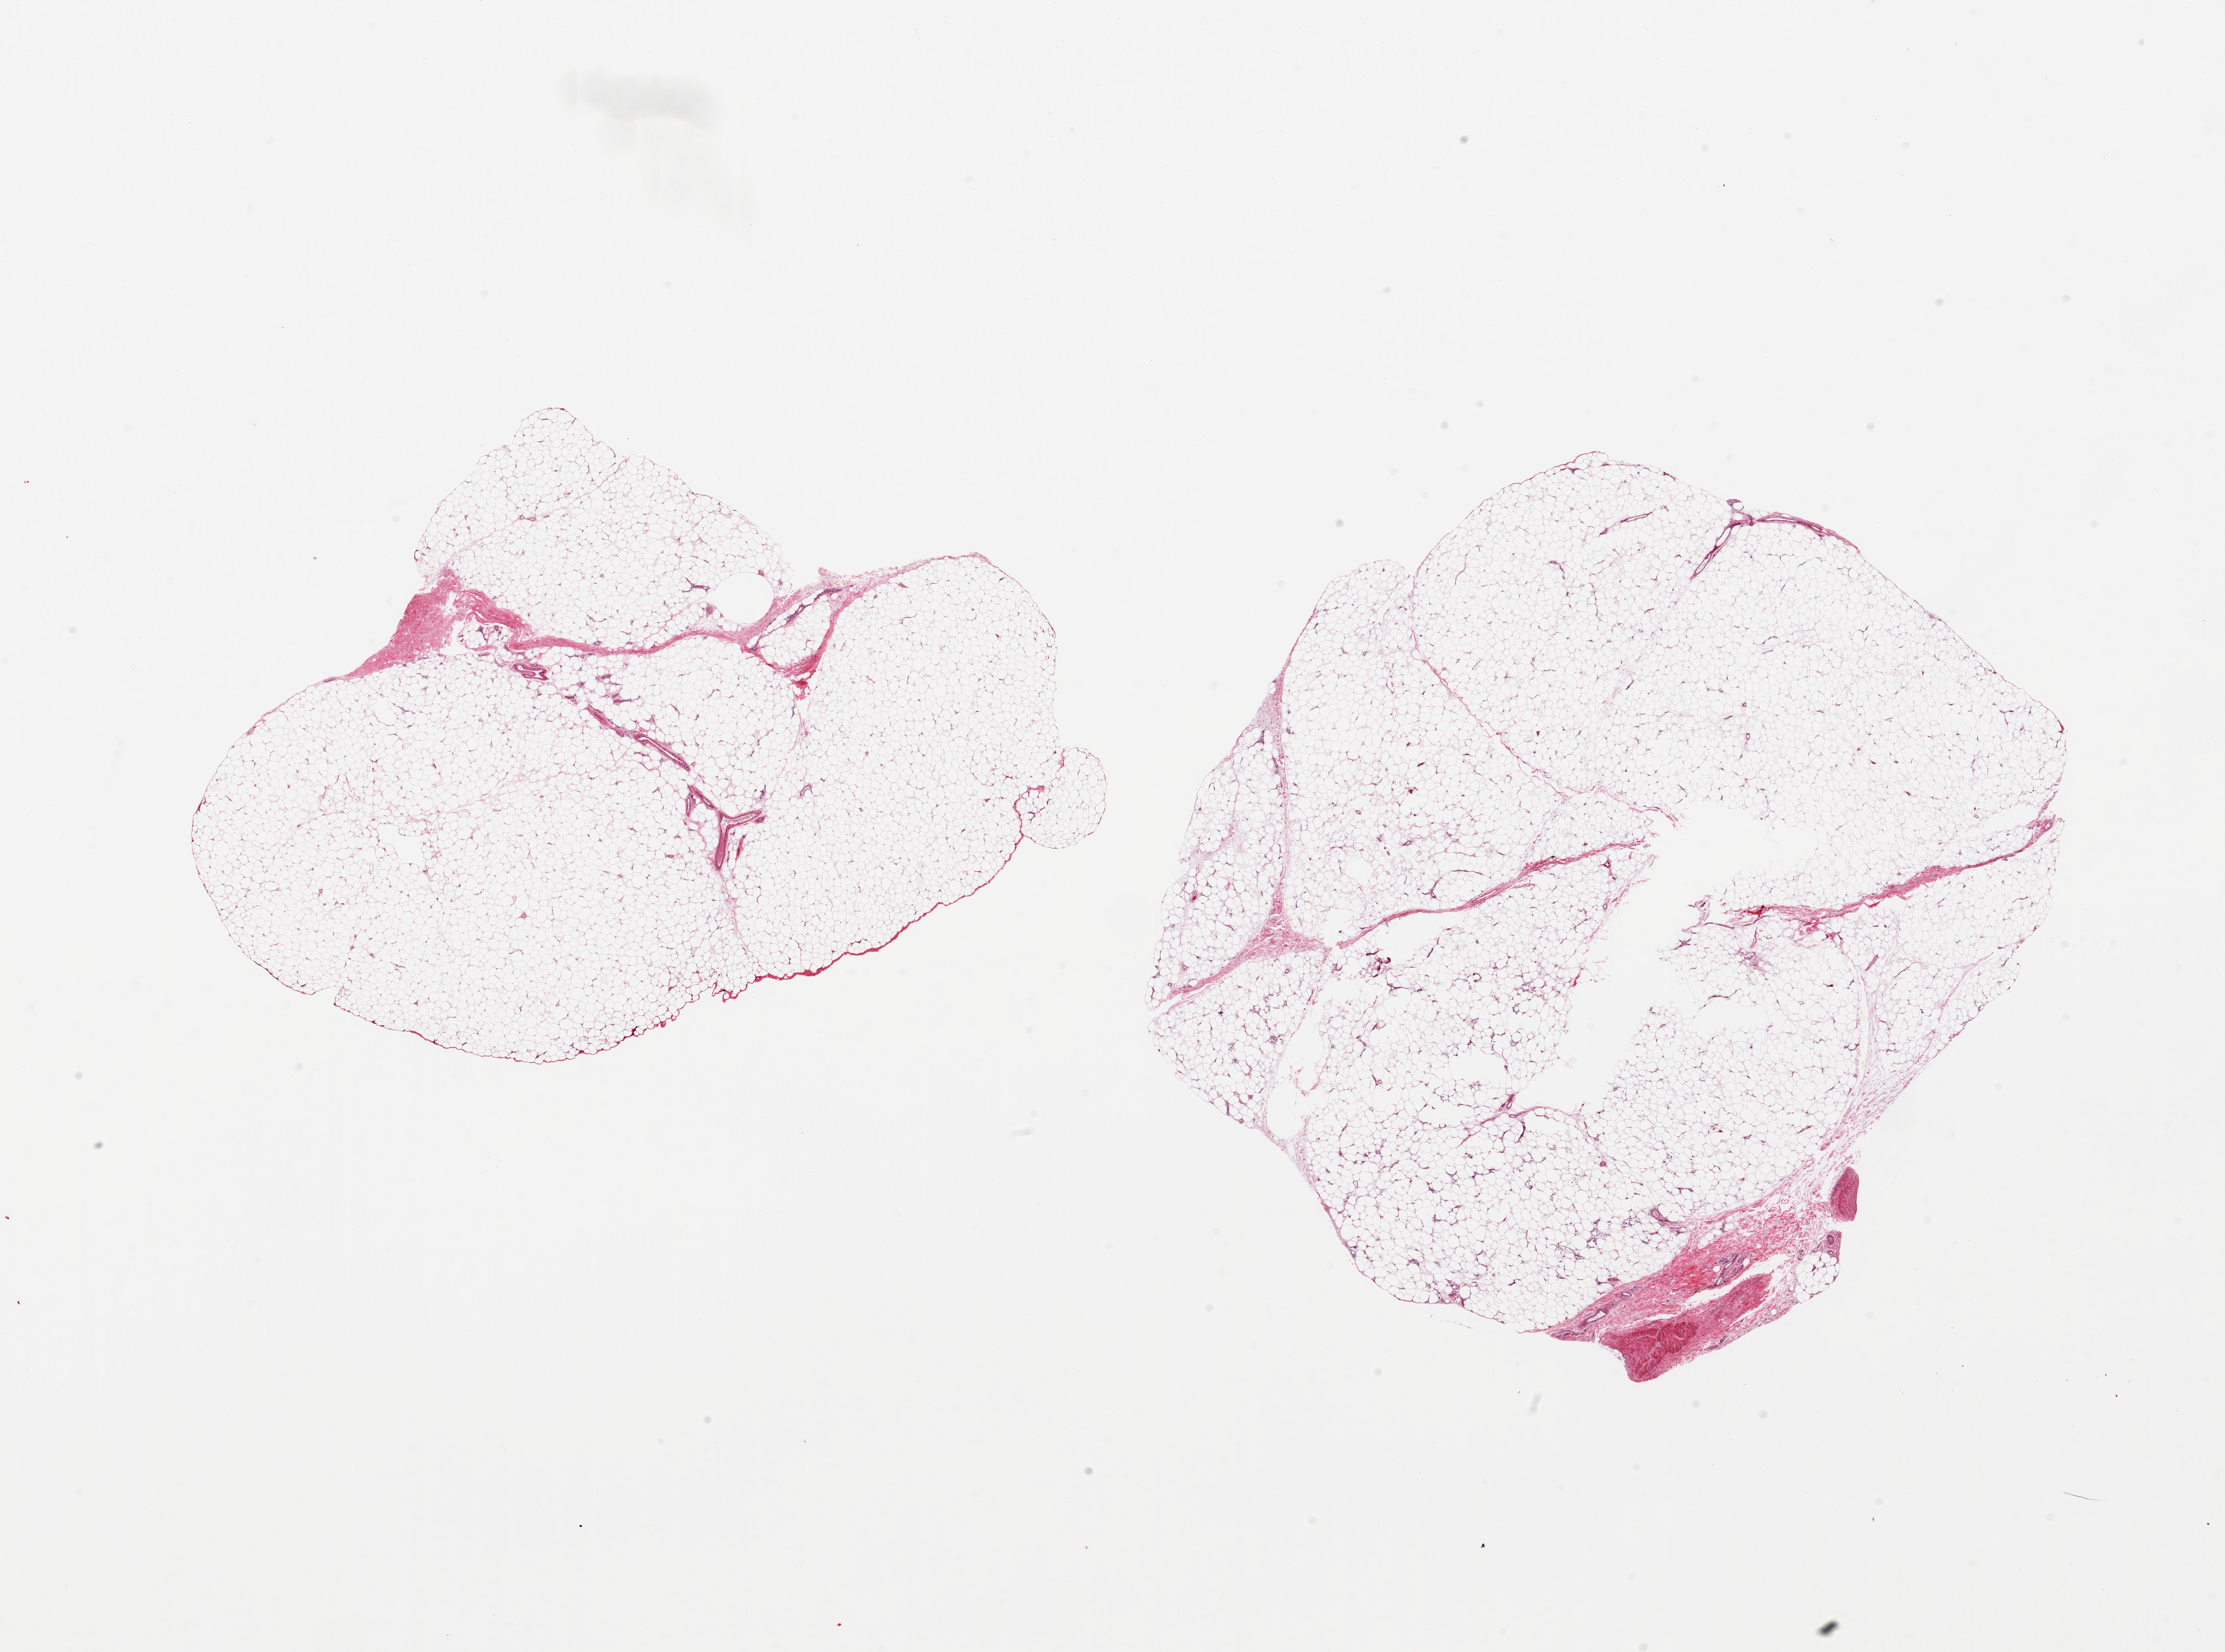
Digitized hematoxylin and eosin (H&E)-stained section, shown as a low-resolution overview of the whole scanned area (about 26.6 x 19.7 mm, slide scanned at 20x); PAXgene-fixed, paraffin-embedded tissue; sampled site (target tissue): adipose tissue; tissue donor sample. Donor sex: male.
Pathologist's review note for this sample: 2 pieces, trace fascia/vascular elements.